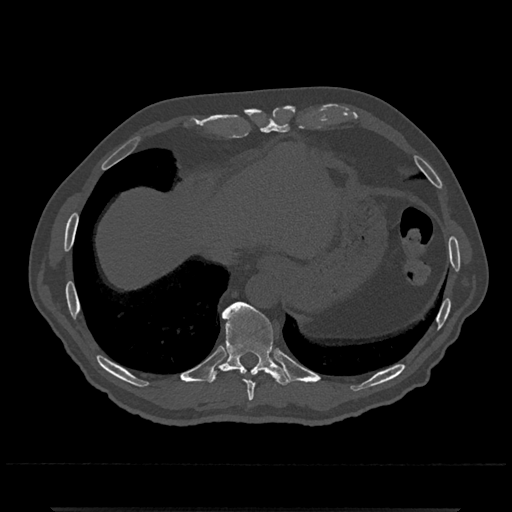
CT including the spine, one axial slice. Position 574 of 797 along the scan axis. Reconstruction kernel Br40s/3. Bone window (W 1800 / L 400 HU). 512 × 512 image matrix, field of view 393 × 393 mm. Patient: male, 67 years. From the clinical record (not read from this slice): primary cancer: prostate.
Outlined on this slice (semi-automatically segmented with operator editing):
- T10 vertebra: box from (x=208, y=301) to (x=290, y=386) px
- T9 vertebra: (x=245, y=380)–(x=255, y=402)